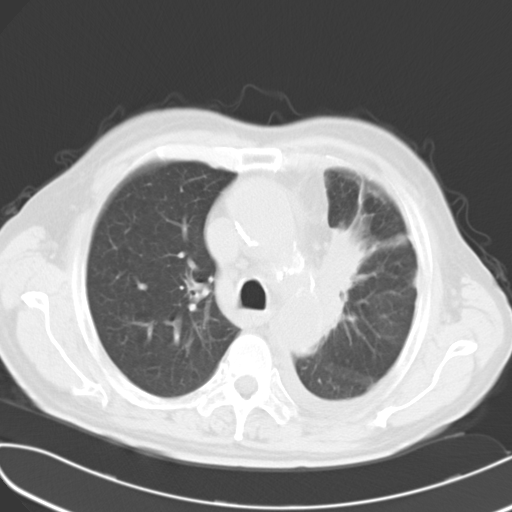
Chest CT, one axial slice; slice 19 of 27 in the series (ordered by position); 120 kVp; lung window (W 1500 / L -600 HU); 10 mm slice thickness; 512 × 512 image matrix, field of view 353 × 353 mm. Male patient, age 70 years. Case-level facts recorded for this patient, not image findings: clinical TNM (as recorded): T2 N1 M3; histopathological grade: G3.
Outlined on this slice (bounding box drawn by a radiologist):
- lung tumour (recorded histology: small cell carcinoma): bounding box <317,220,357,339> (left, top, right, bottom; pixels)